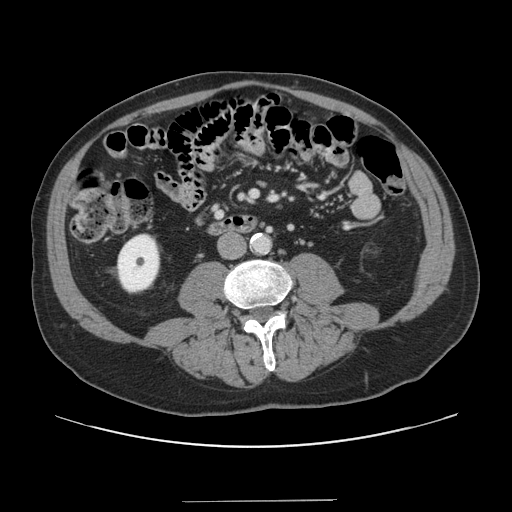
Contrast-enhanced abdominal CT, one axial slice. Slice 21 of 151 in the series (ordered by position). Intravenous contrast given. Soft-tissue window (W 400 / L 40 HU). 512 × 512 image matrix. Male patient, age 63 years. From the clinical record (not read from this slice): diagnosis: colorectal cancer liver metastases, imaged before liver resection; multiple liver metastases: no; largest metastasis: 2.1 cm; chemotherapy before resection: no.
Outlined on this slice (outlined manually by an expert reader):
- portal vein (with intrahepatic branches): bounding box (x1, y1, x2, y2) in pixels: (253, 192, 255, 194)